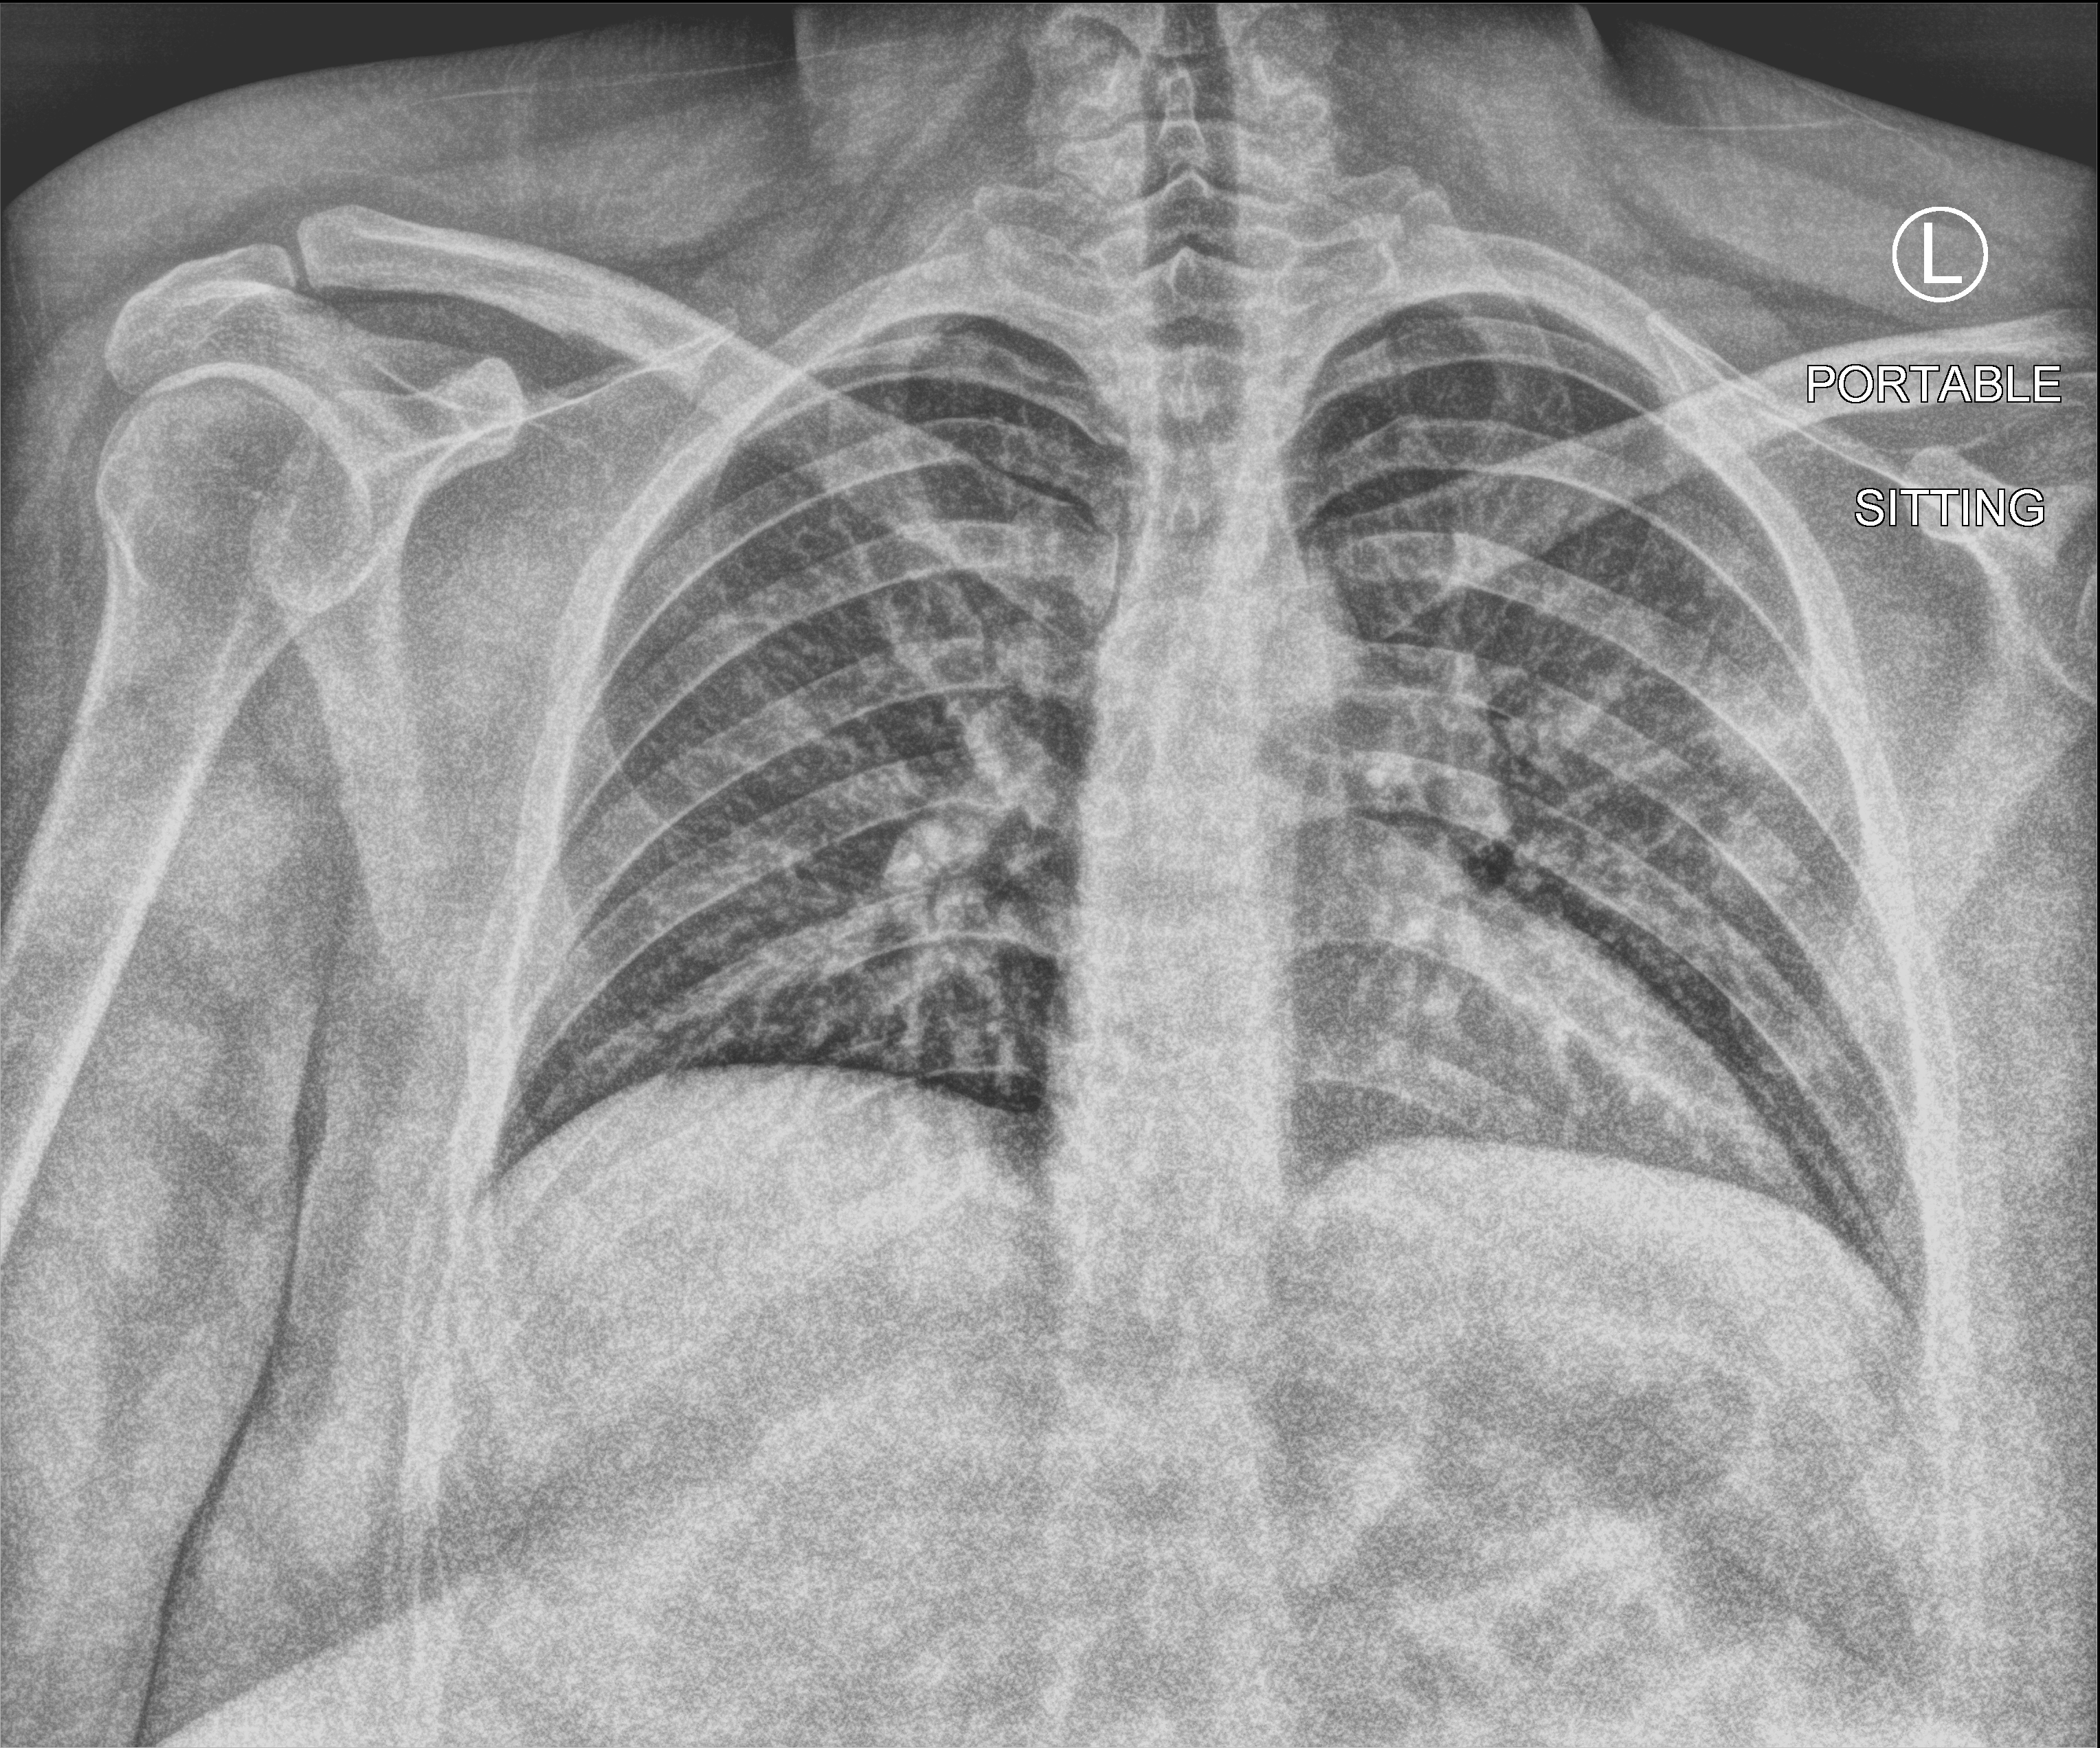
Chest X-ray (portable), anteroposterior (AP) projection. Patient hospitalised with COVID-19; female, aged 18–59 years.
From the hospital-stay record, not from the radiograph (when in the stay this image was taken is not recorded):
- admitted to intensive care during this hospital stay: no